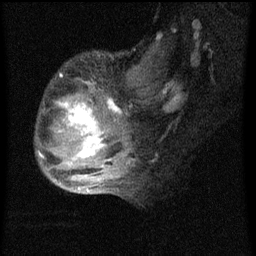
Breast MRI (dynamic contrast-enhanced), one sagittal slice. Position 22 of 60 along the scan axis. Dynamic contrast-enhanced series, image 2 of 4 at this slice position (ordered by acquisition). 1.5 T. TE 4.2 ms, TR 8 ms. 2 mm slice thickness. 256 × 256 image matrix, field of view 180 × 180 mm. Female patient, age 50 years.
Outlined on this slice (semi-automatically segmented with operator editing):
- analysis volume of interest (the breast-tissue region the enhancement analysis was run in; not a lesion): bounding box <36,64,124,177> (left, top, right, bottom; pixels)
- tumour enhancement mask (voxels above the 70 % enhancement threshold inside the analysis volume of interest): <42,98,122,177>